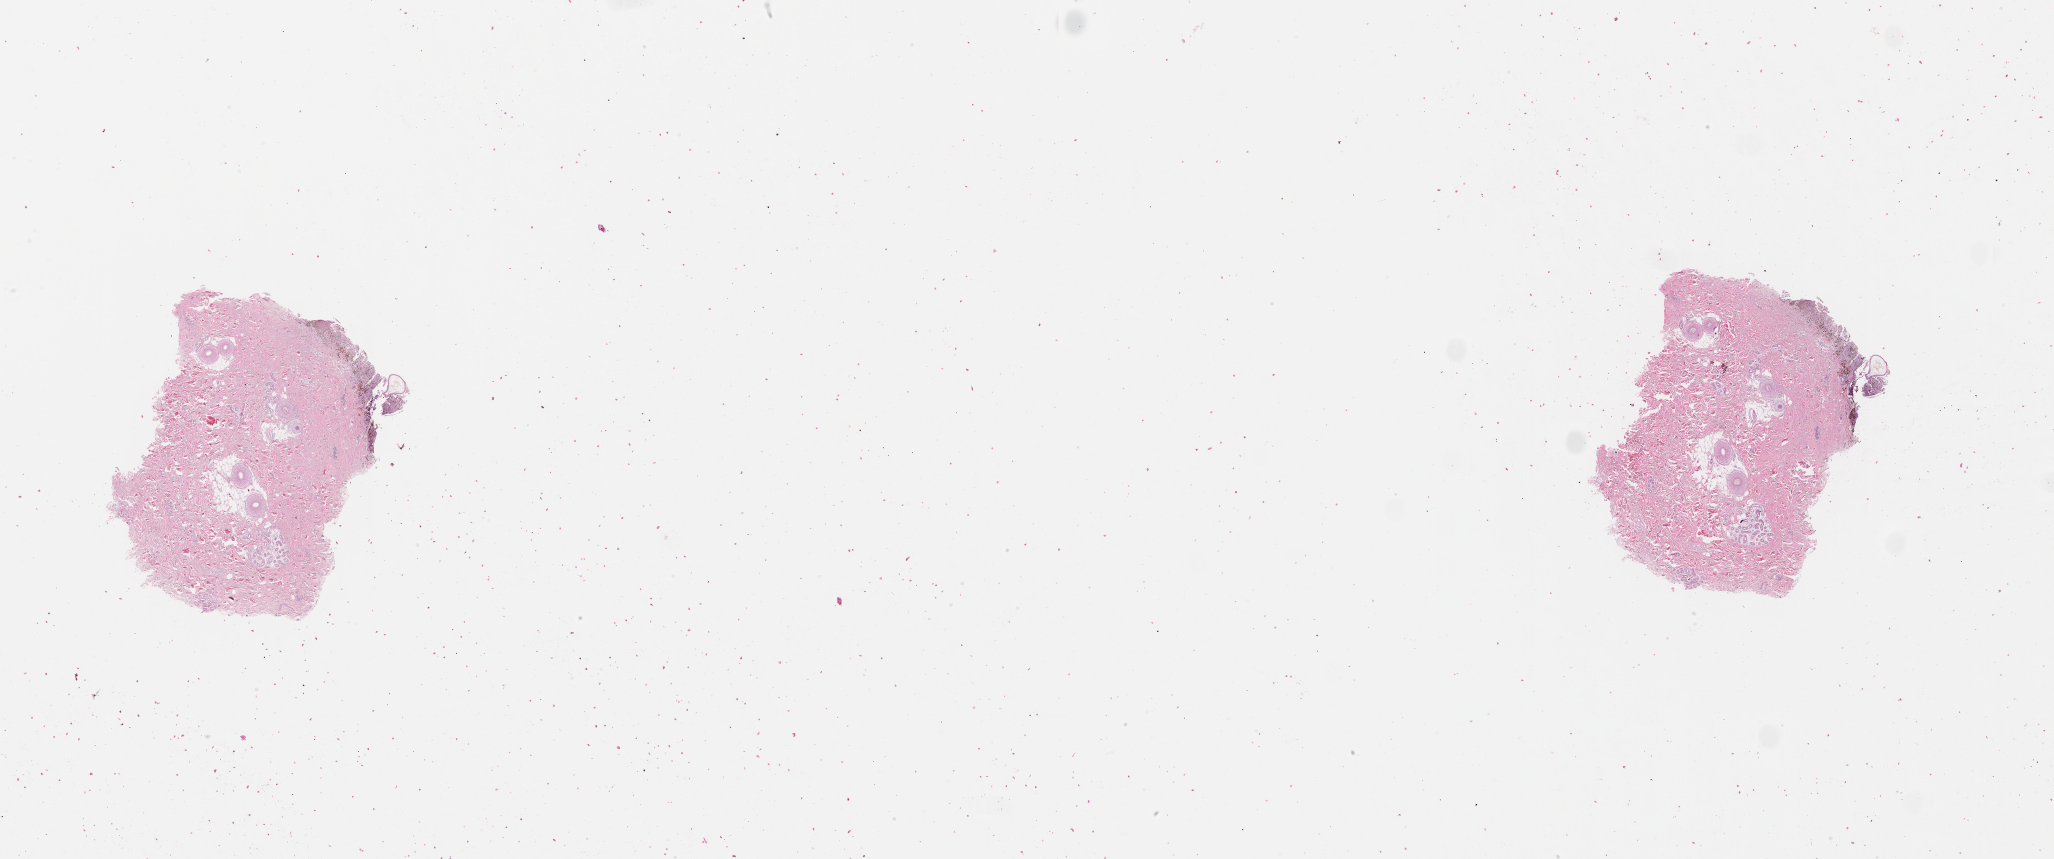
Whole-slide histology image, Hematoxylin and eosin (H&E) stained — a low-resolution overview of the entire scanned area, about 33.1 x 13.8 mm (from a 20x scan). 61-year-old male patient.
Patient diagnosis: Malignant melanoma, NOS.